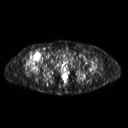
FDG PET of an extremity soft-tissue mass (from a PET/CT study), one axial slice. Slice 282 of 311 in the series (ordered by position). 3.27 mm slice thickness. 128 × 128 image matrix, field of view 500 × 500 mm. Patient: female, 57 years. From the clinical record (not read from this slice): histological type: pleiomorphic undifferentiated sarcoma; grade: high; site of the primary tumour: right quadricep.
Annotated regions visible in this slice (expert contour drawn on MRI and transferred to this co-registered scan by the dataset authors):
- tumour plus oedema (research contour): bounding box [x1, y1, x2, y2] px = [25, 51, 42, 69]
- tumour (research contour): [28, 51, 42, 63]